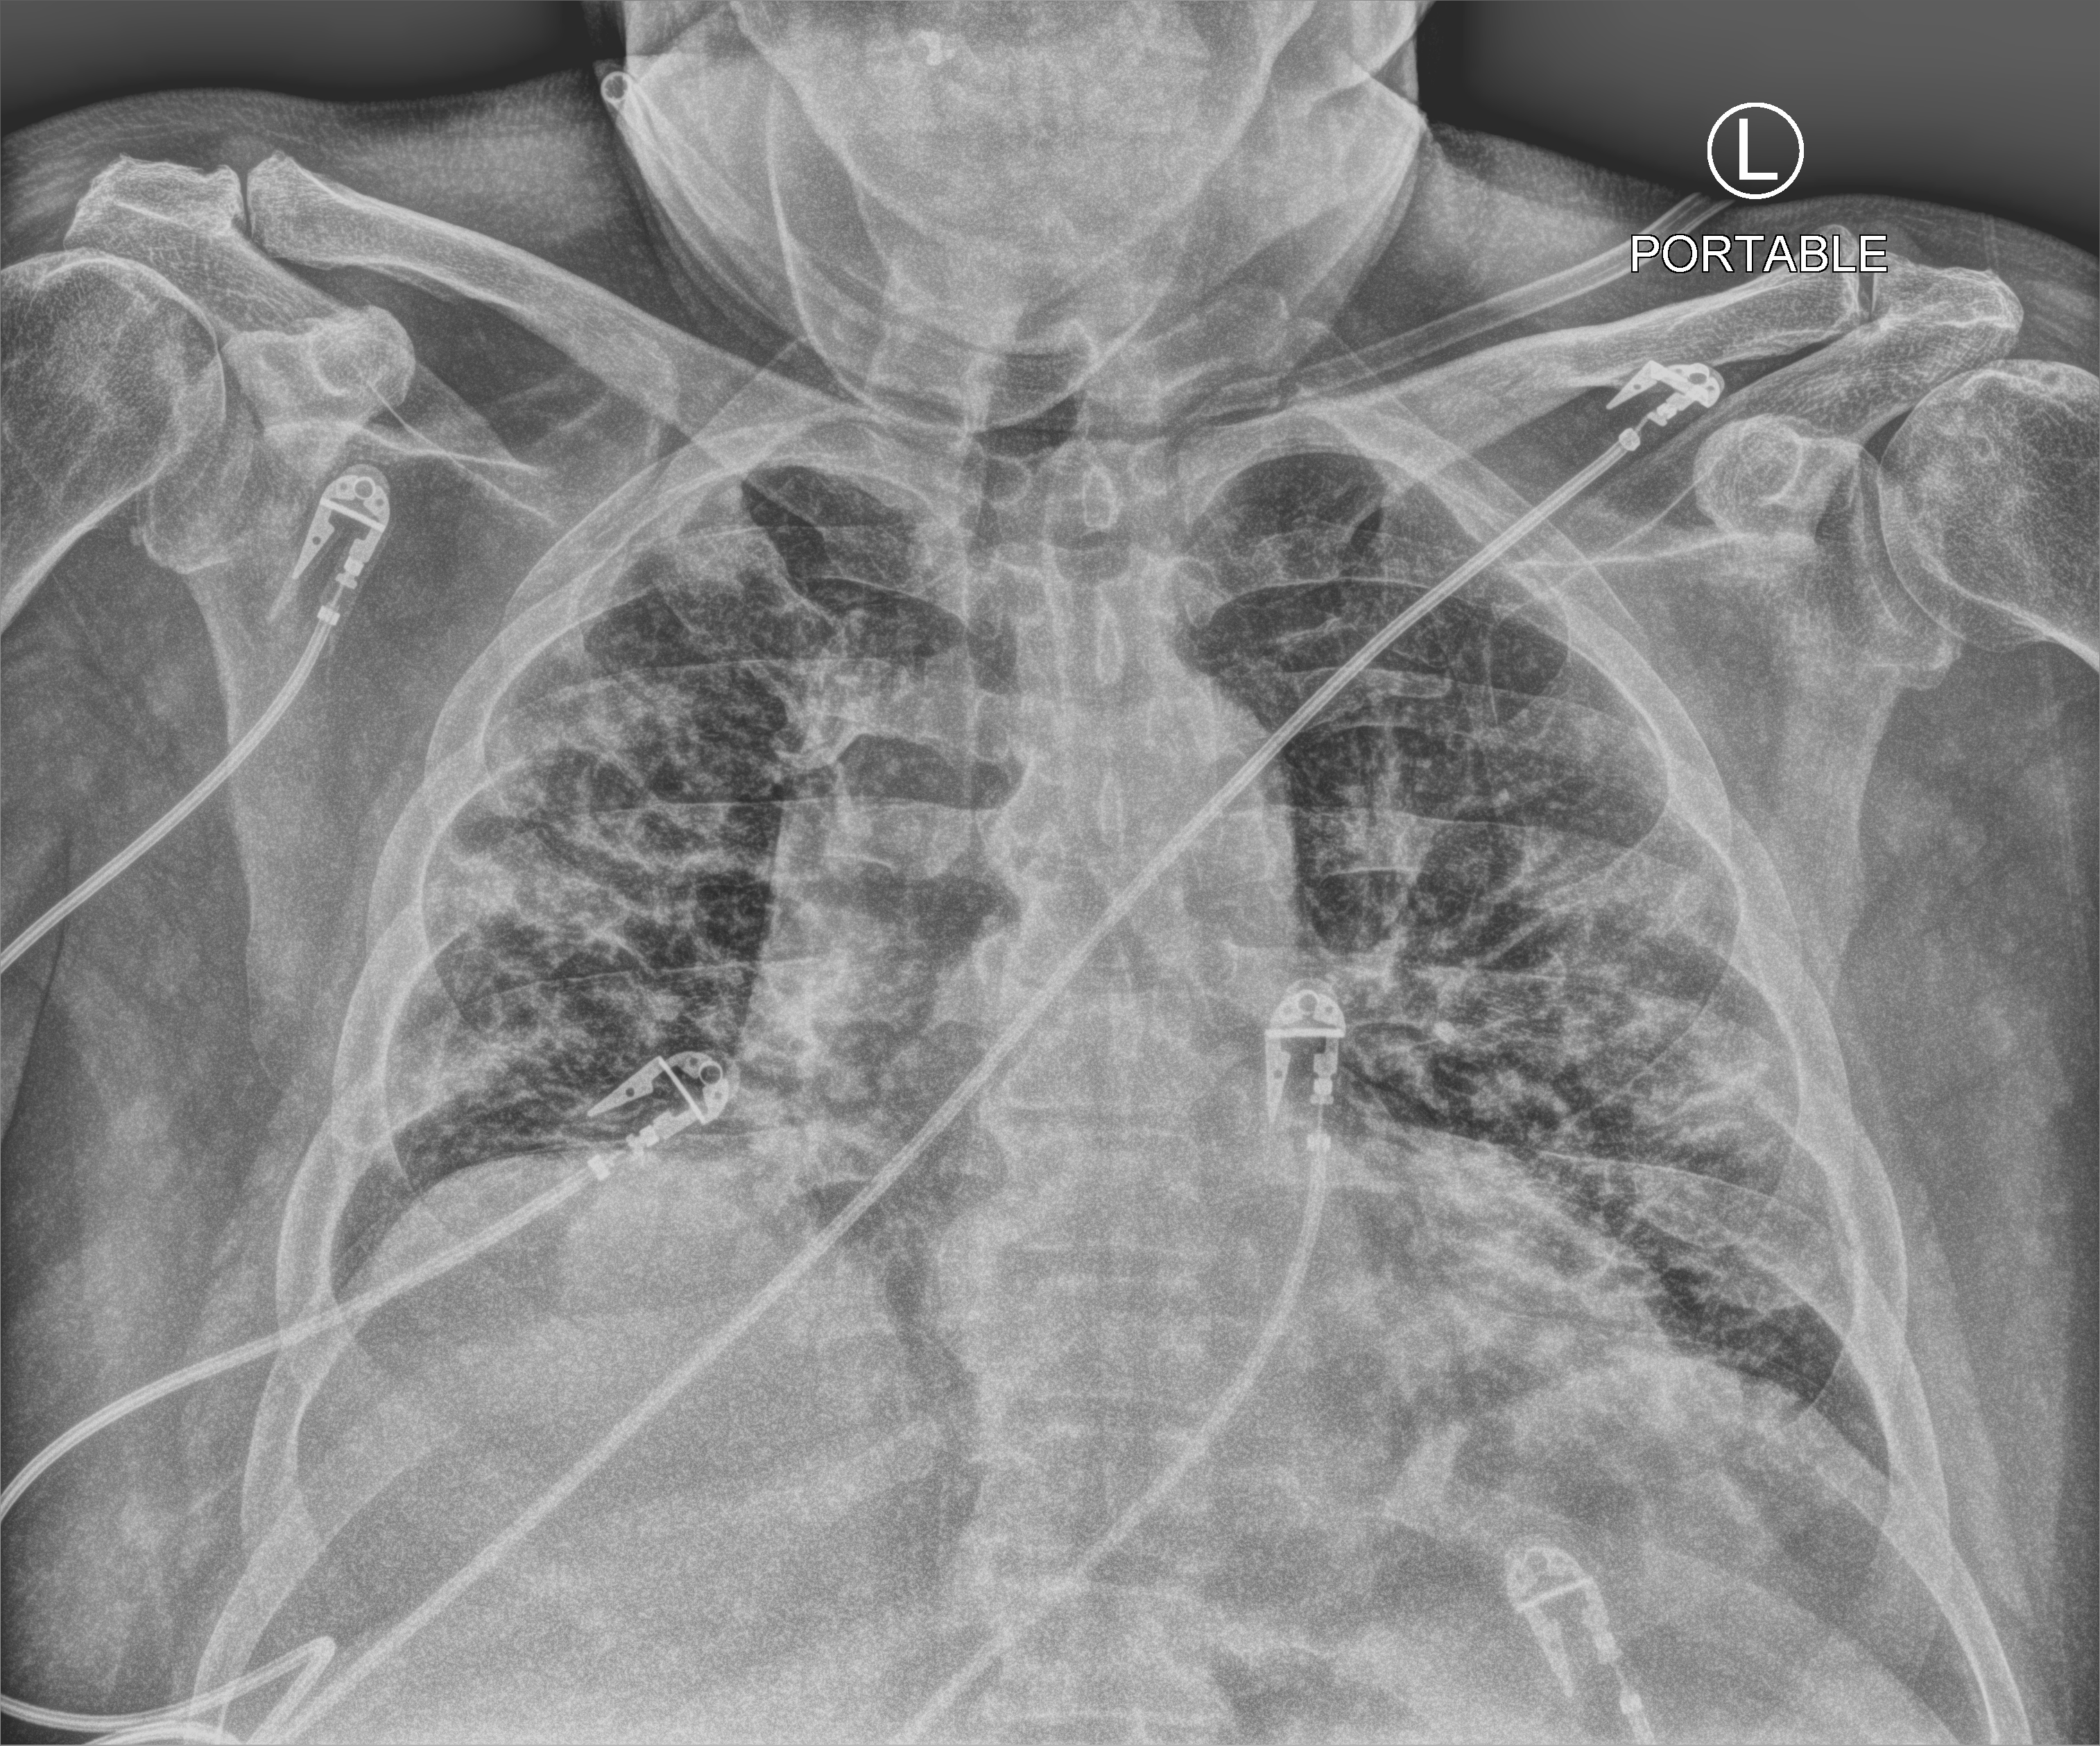
Chest X-ray (portable). Male patient hospitalised with COVID-19, age 60–74 years.
Hospital-stay facts (about this admission, not read from this image; timing relative to this image not recorded): mechanically ventilated during this hospital stay: no; length of hospital stay: 10 days.